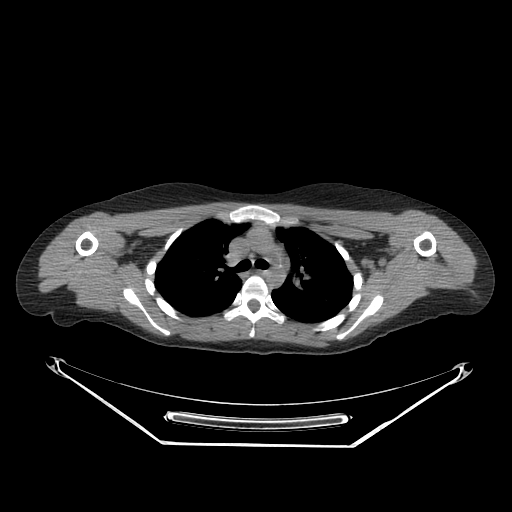
CT of an extremity soft-tissue mass (from a PET/CT study), one axial slice. Position 202 of 267 along the scan axis. Reconstruction kernel SOFT. 140 kVp. Soft-tissue window (W 400 / L 40 HU). 3.75 mm slice thickness. 512 × 512 image matrix, field of view 500 × 500 mm. Female patient. From the clinical record (not read from this slice): histological type: malignant fibrous histiocytoma; grade: low; site of the primary tumour: left arm.
Annotated regions visible in this slice (expert contour drawn on MRI and transferred to this co-registered scan by the dataset authors):
- gross tumour volume (mass): box from (x=427, y=251) to (x=457, y=280) px